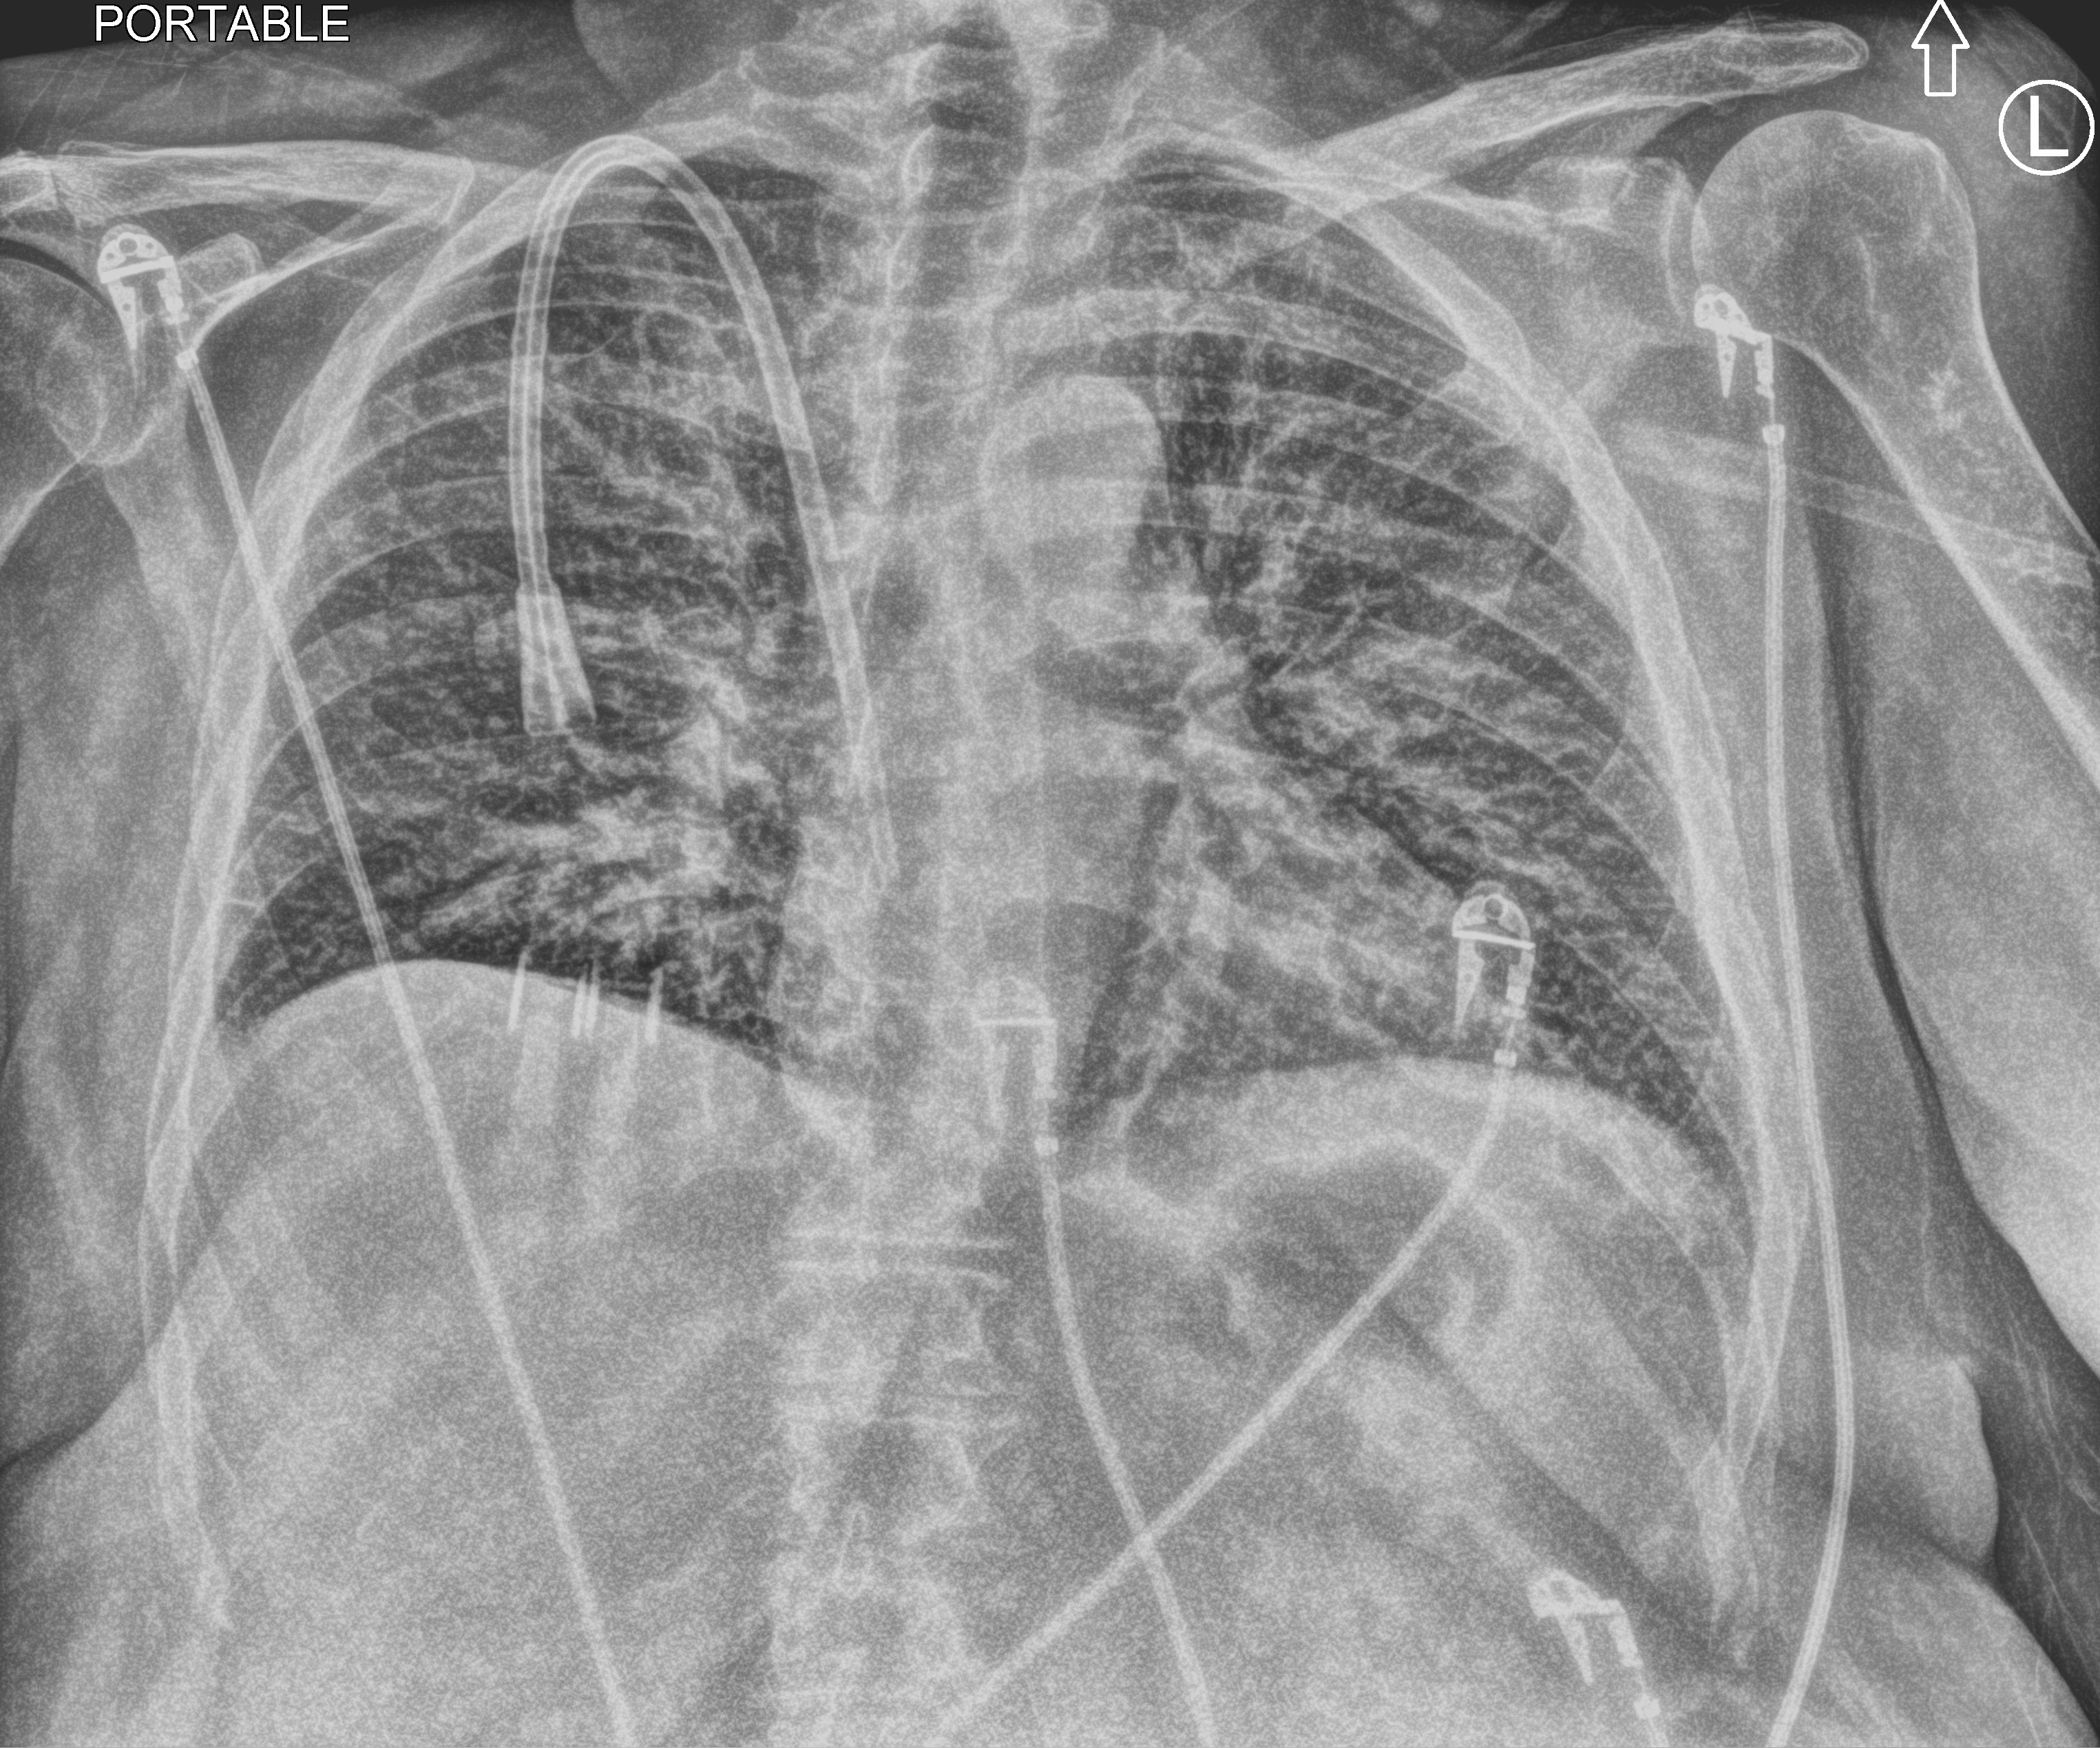
Chest X-ray (portable); anteroposterior (AP) projection. Patient hospitalised with COVID-19; female, aged 60–74 years.
From the hospital-stay record, not from the radiograph (when in the stay this image was taken is not recorded): mechanically ventilated during this hospital stay: no.